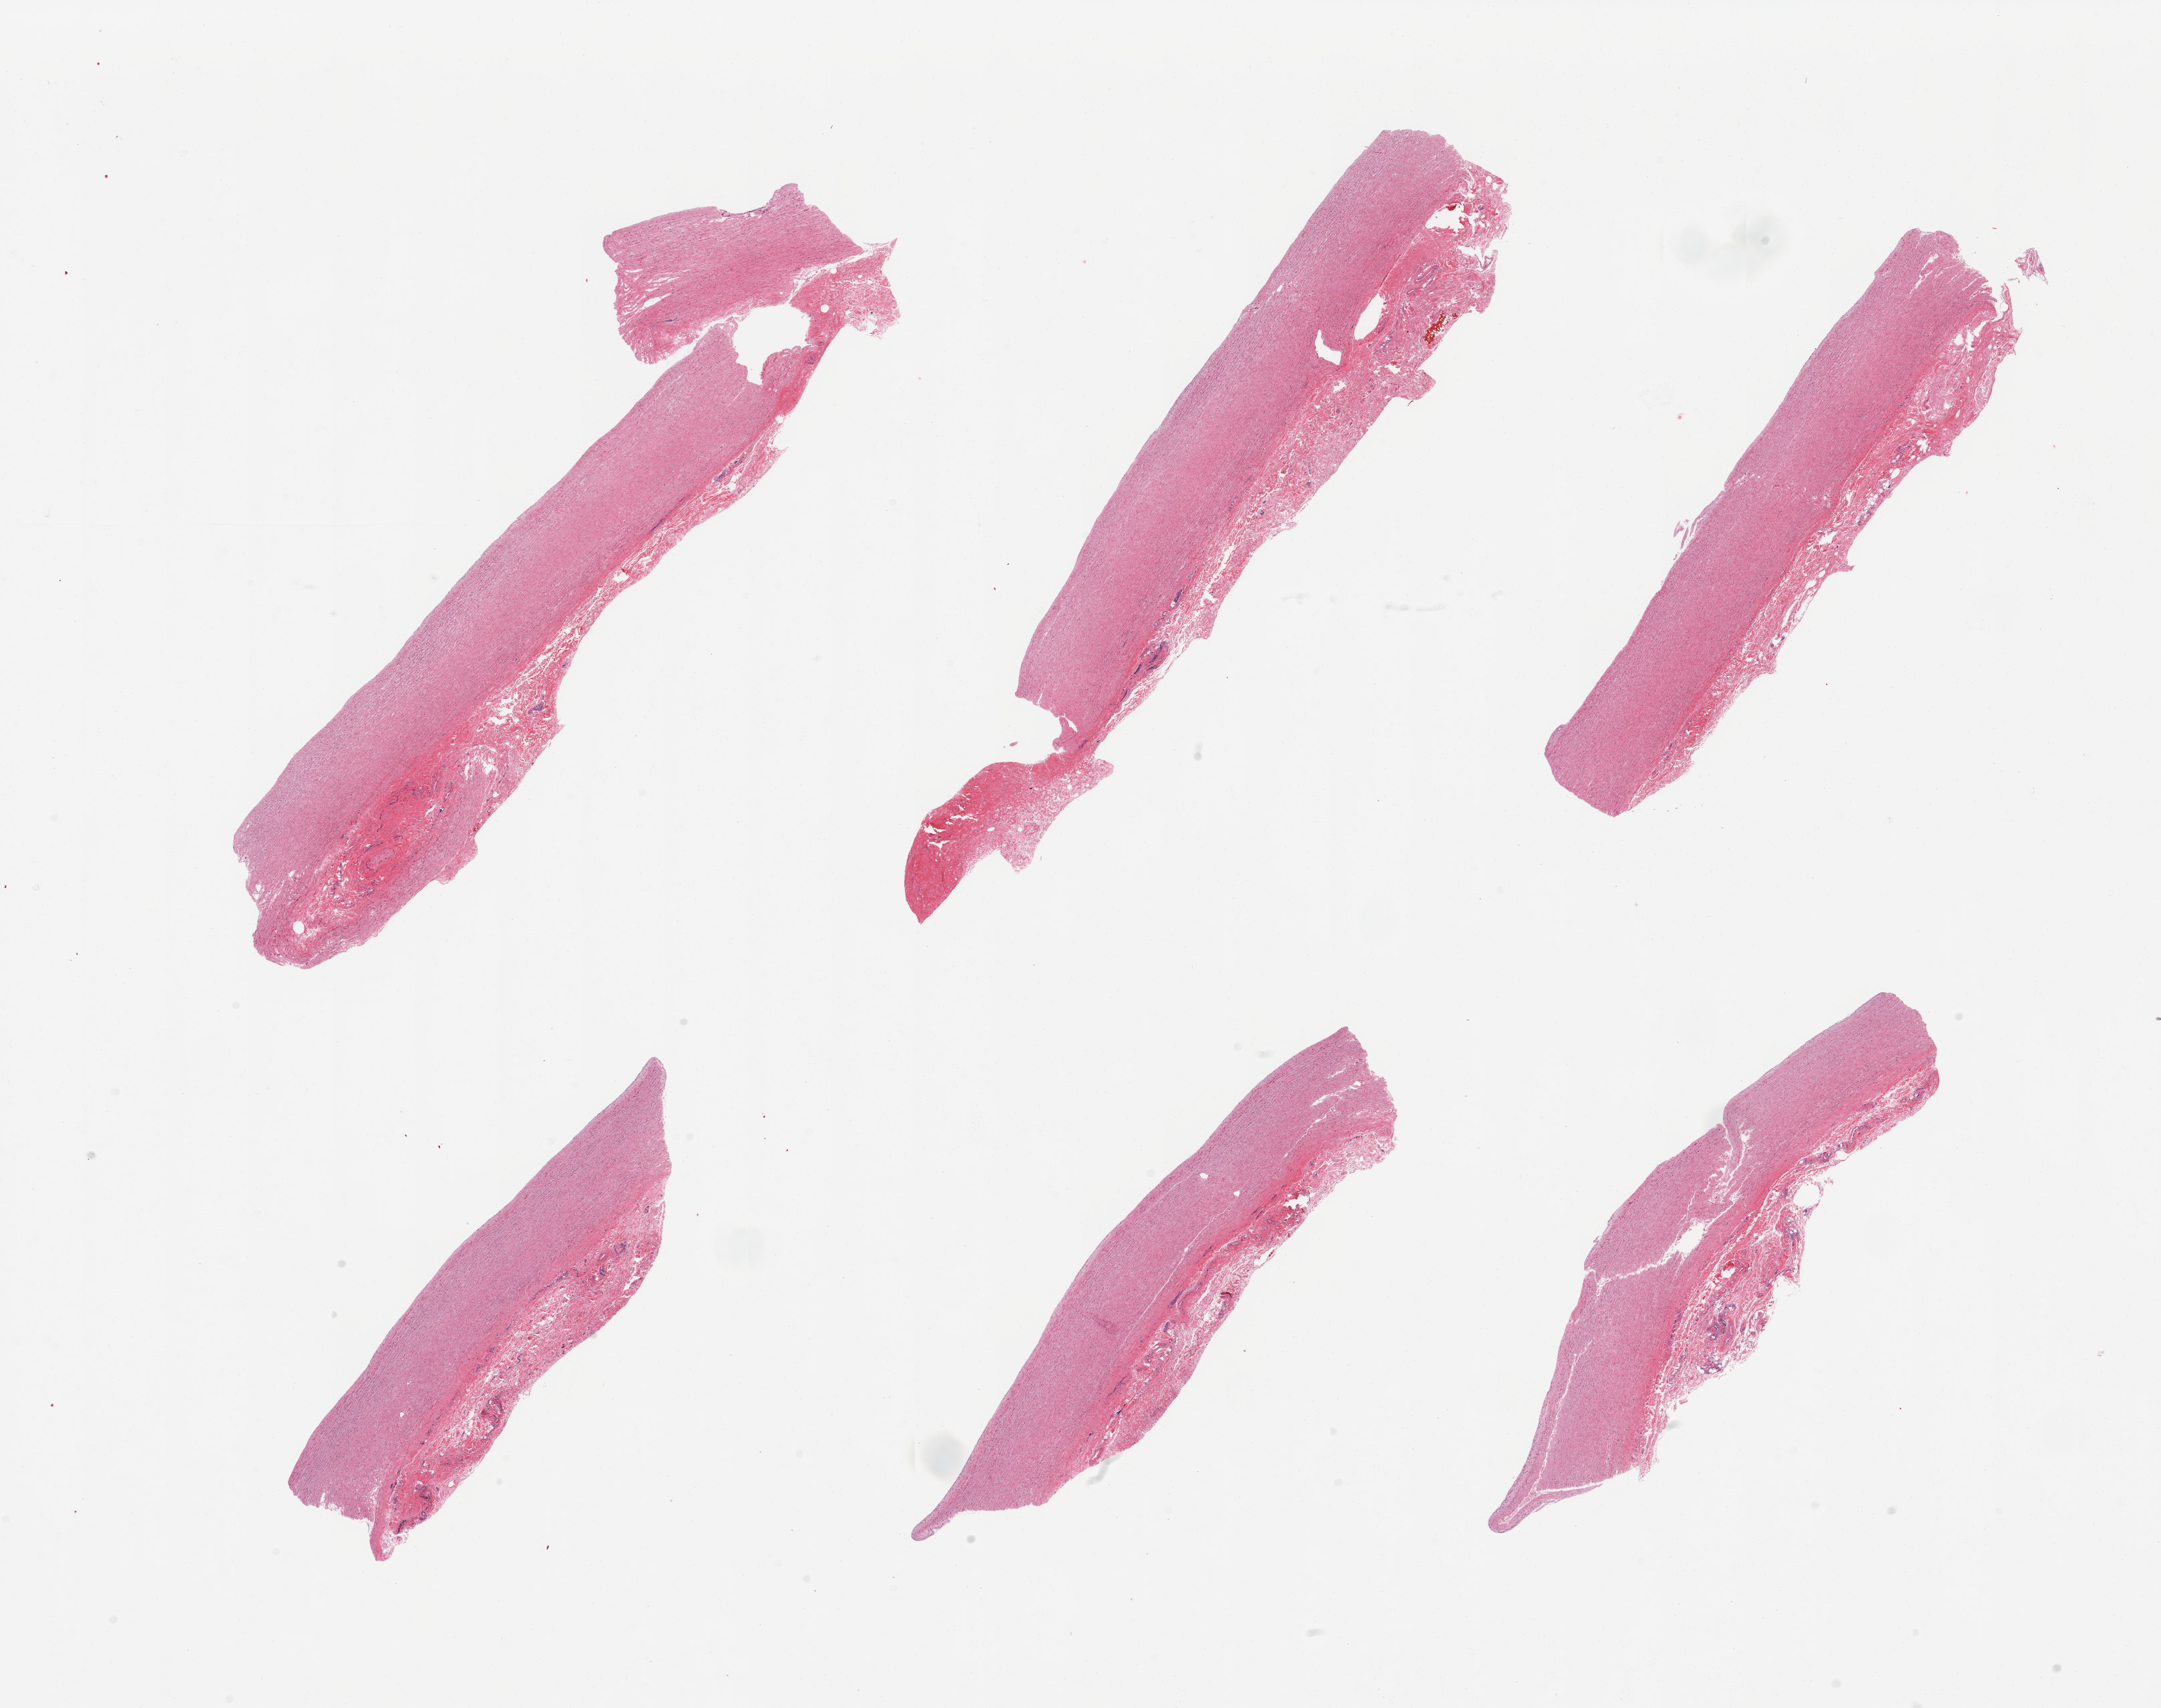
Whole-slide image, hematoxylin and eosin (H&E) stain — a low-resolution overview of the entire scanned area, about 25.6 x 20.2 mm (slide scanned at 20x), PAXgene-fixed paraffin-embedded (PFPE) section, target tissue: aorta, donor tissue sample. Female donor.
Reviewer comment on this tissue sample: 6 pieces; adventitia up to 1mm thick.